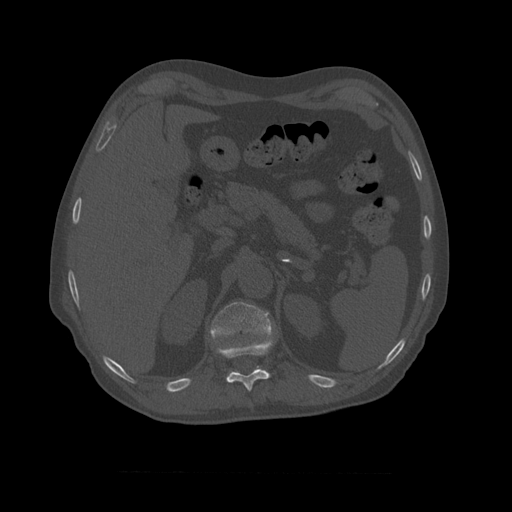
CT including the spine, one axial slice. Slice 395 of 450 in the series (ordered by position). Reconstruction kernel STANDARD. 120 kVp. Bone window (W 1800 / L 400 HU). 1.25 mm slice thickness. 512 × 512 image matrix. Patient age 75 years. From the clinical record (not read from this slice): primary cancer: prostate.
Outlined on this slice (semi-automatic segmentation, software-assisted and operator-edited):
- T10 vertebra: bounding box [x1, y1, x2, y2] px = [216, 339, 273, 392]
- T11 vertebra: [209, 302, 275, 372]